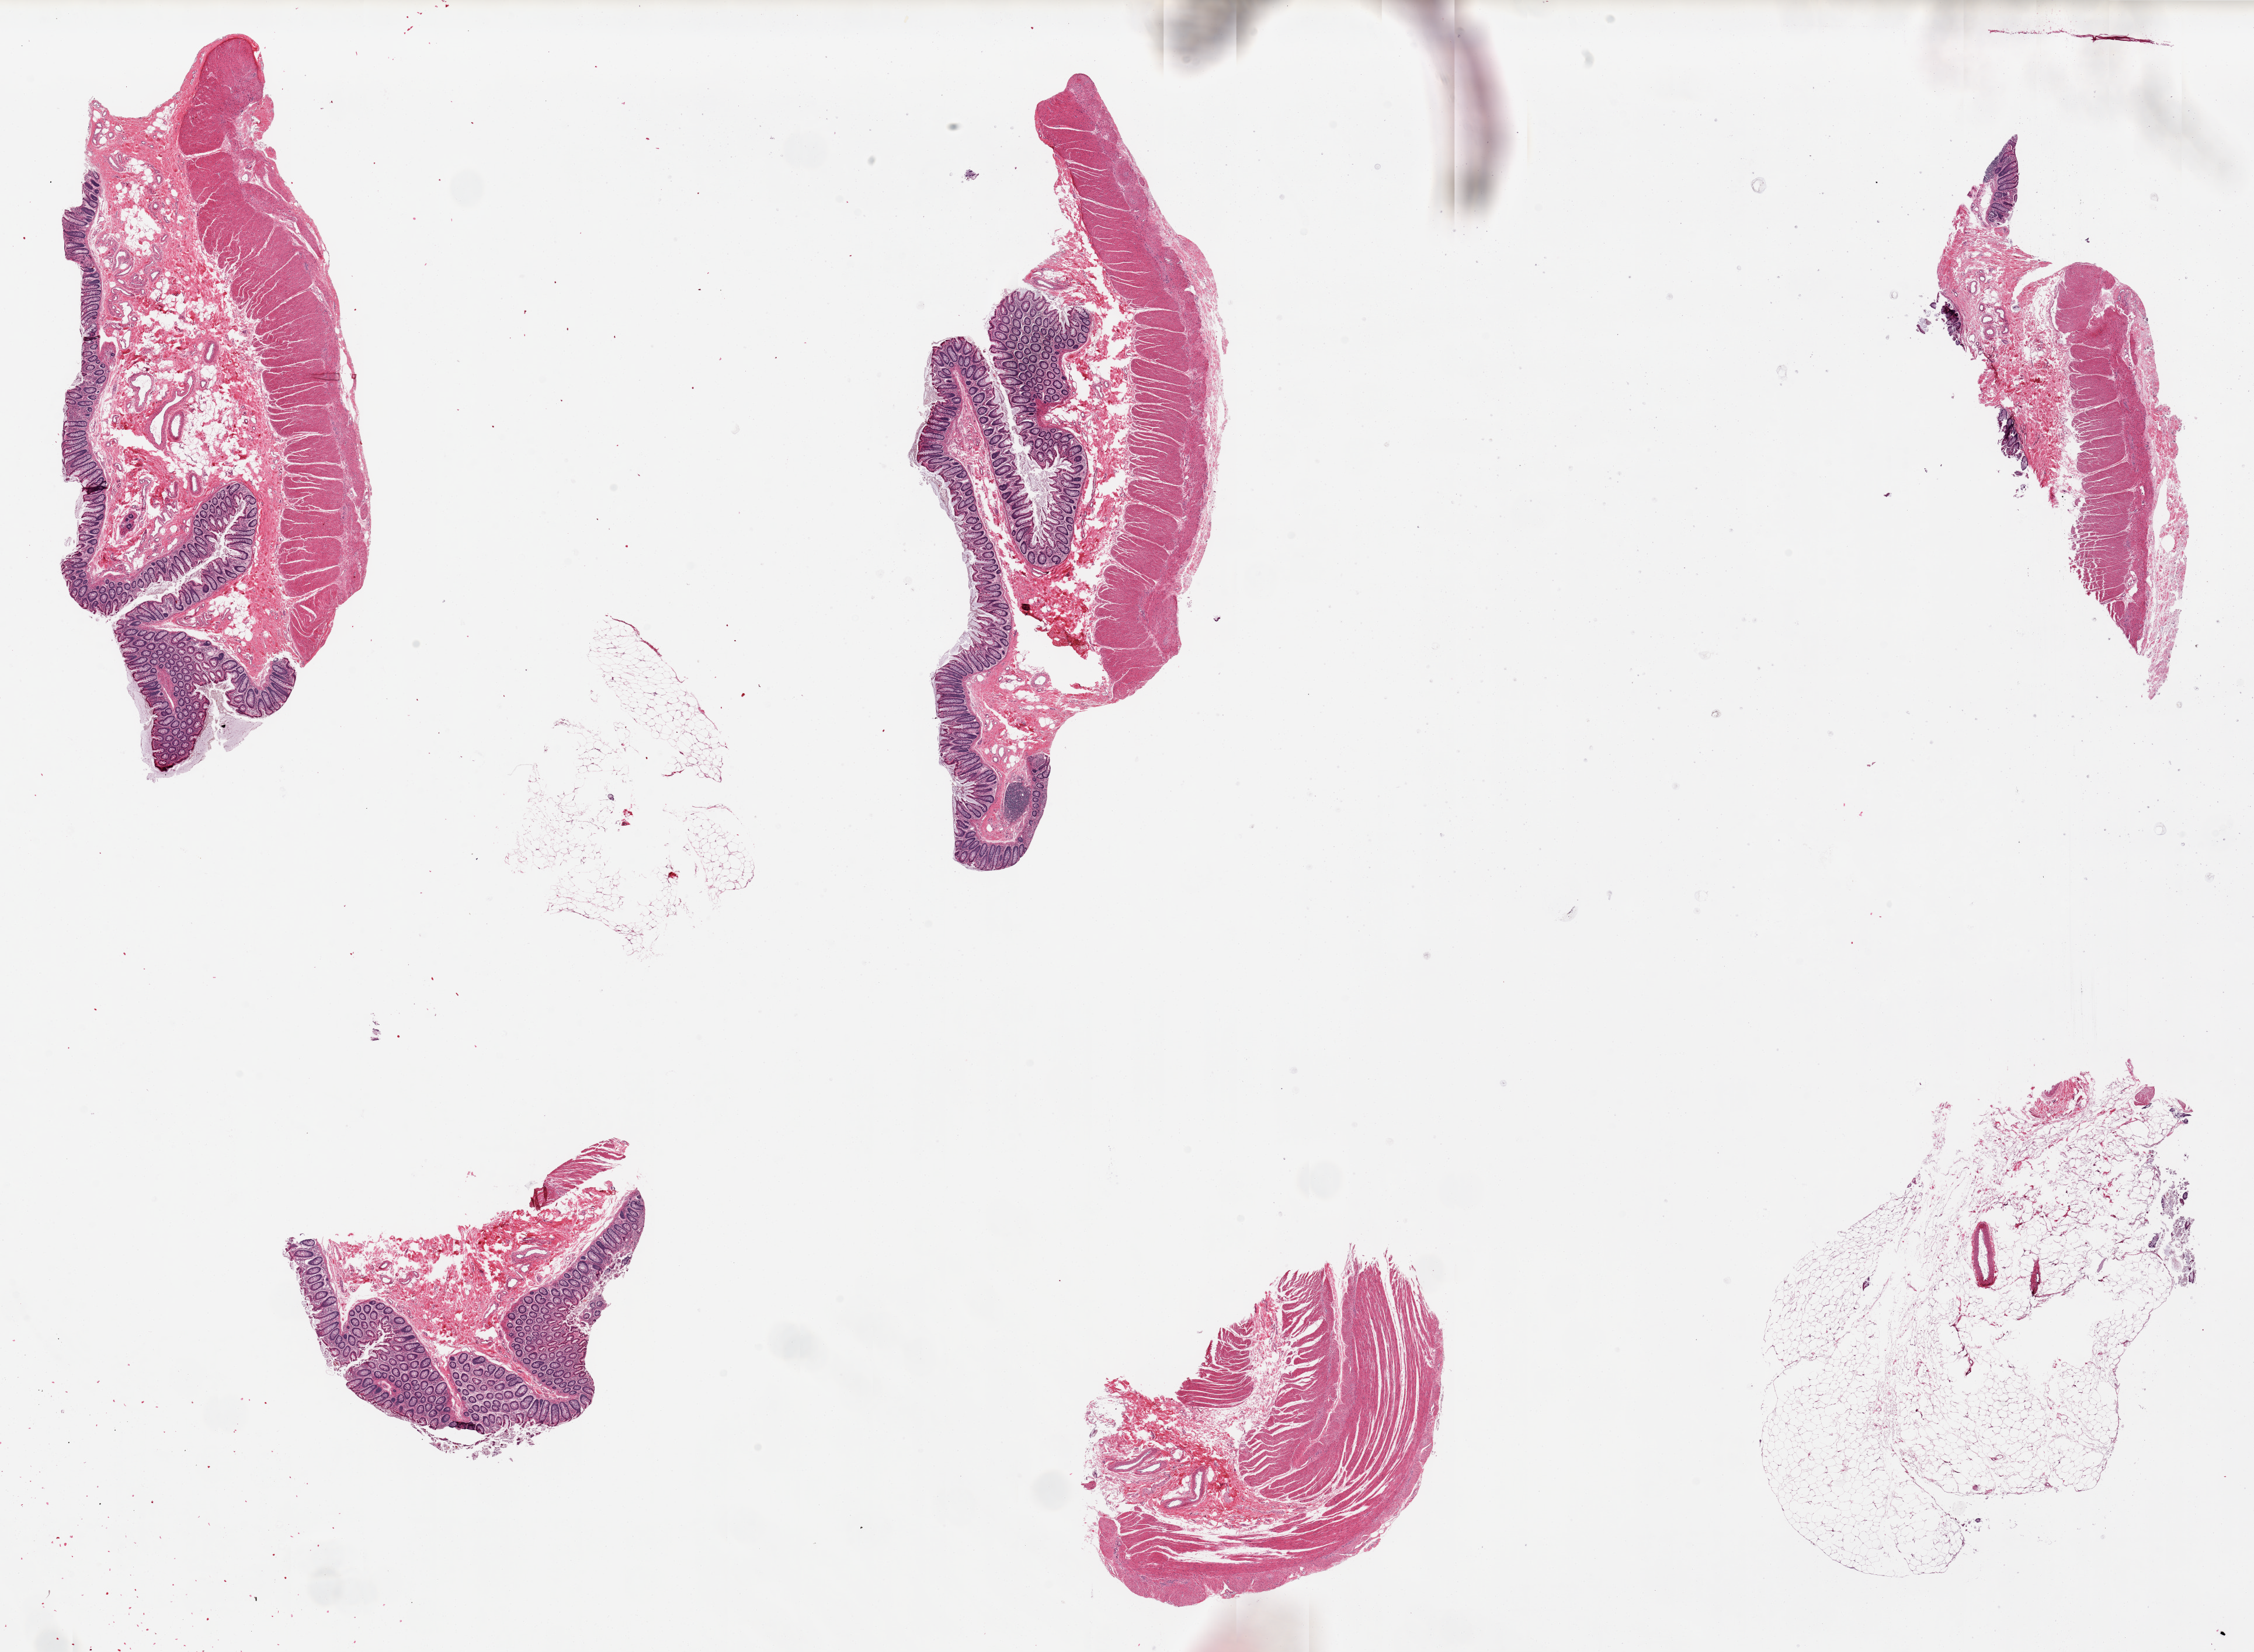
H&E whole-slide image, a low-resolution overview of the entire scanned area, about 30.5 x 22.4 mm (acquisition: 20x scan). PAXgene-fixed, paraffin-embedded tissue. Sampled site (target tissue): transverse colon. Donor tissue sample. Male donor.
Reviewer comment on this tissue sample: 6 pieces, up to 11x4mm; 3 with good mucosa; 4 with muscularis; 1 with only adipose.